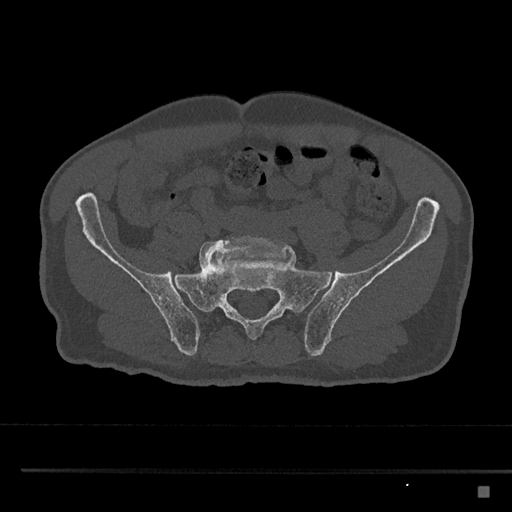
CT including the spine, one axial slice; position 539 of 797 along the scan axis; reconstruction kernel Br40s/3; 120 kVp; bone window (W 1800 / L 400 HU); 0.5 mm slice thickness; 512 × 512 image matrix. Patient: male, 59 years. From the clinical record (not read from this slice): primary cancer: prostate.
Structures marked on this image (semi-automatically segmented with operator editing):
- L5 vertebra: bounding box [x1, y1, x2, y2] px = [199, 235, 291, 271]